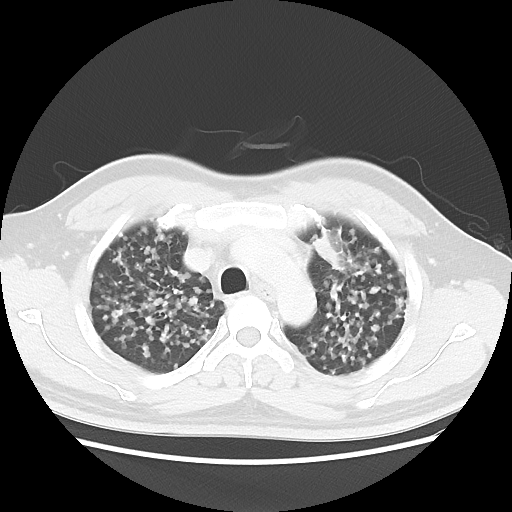
Chest CT, one axial slice; slice 30 of 40 in the series (ordered by position); reconstruction kernel LUNG; 120 kVp; lung window (W 1500 / L -600 HU); 5 mm slice thickness; 512 × 512 image matrix, field of view 366 × 366 mm. Male patient, age 41 years. Case-level facts recorded for this patient, not image findings: clinical TNM (as recorded): T1c N3 M1b; histopathological grade: G2-3.
Structures marked on this image (rectangle marked by the reading radiologist):
- lung tumour (recorded histology: adenocarcinoma): bounding box [x1, y1, x2, y2] px = [309, 221, 349, 278]